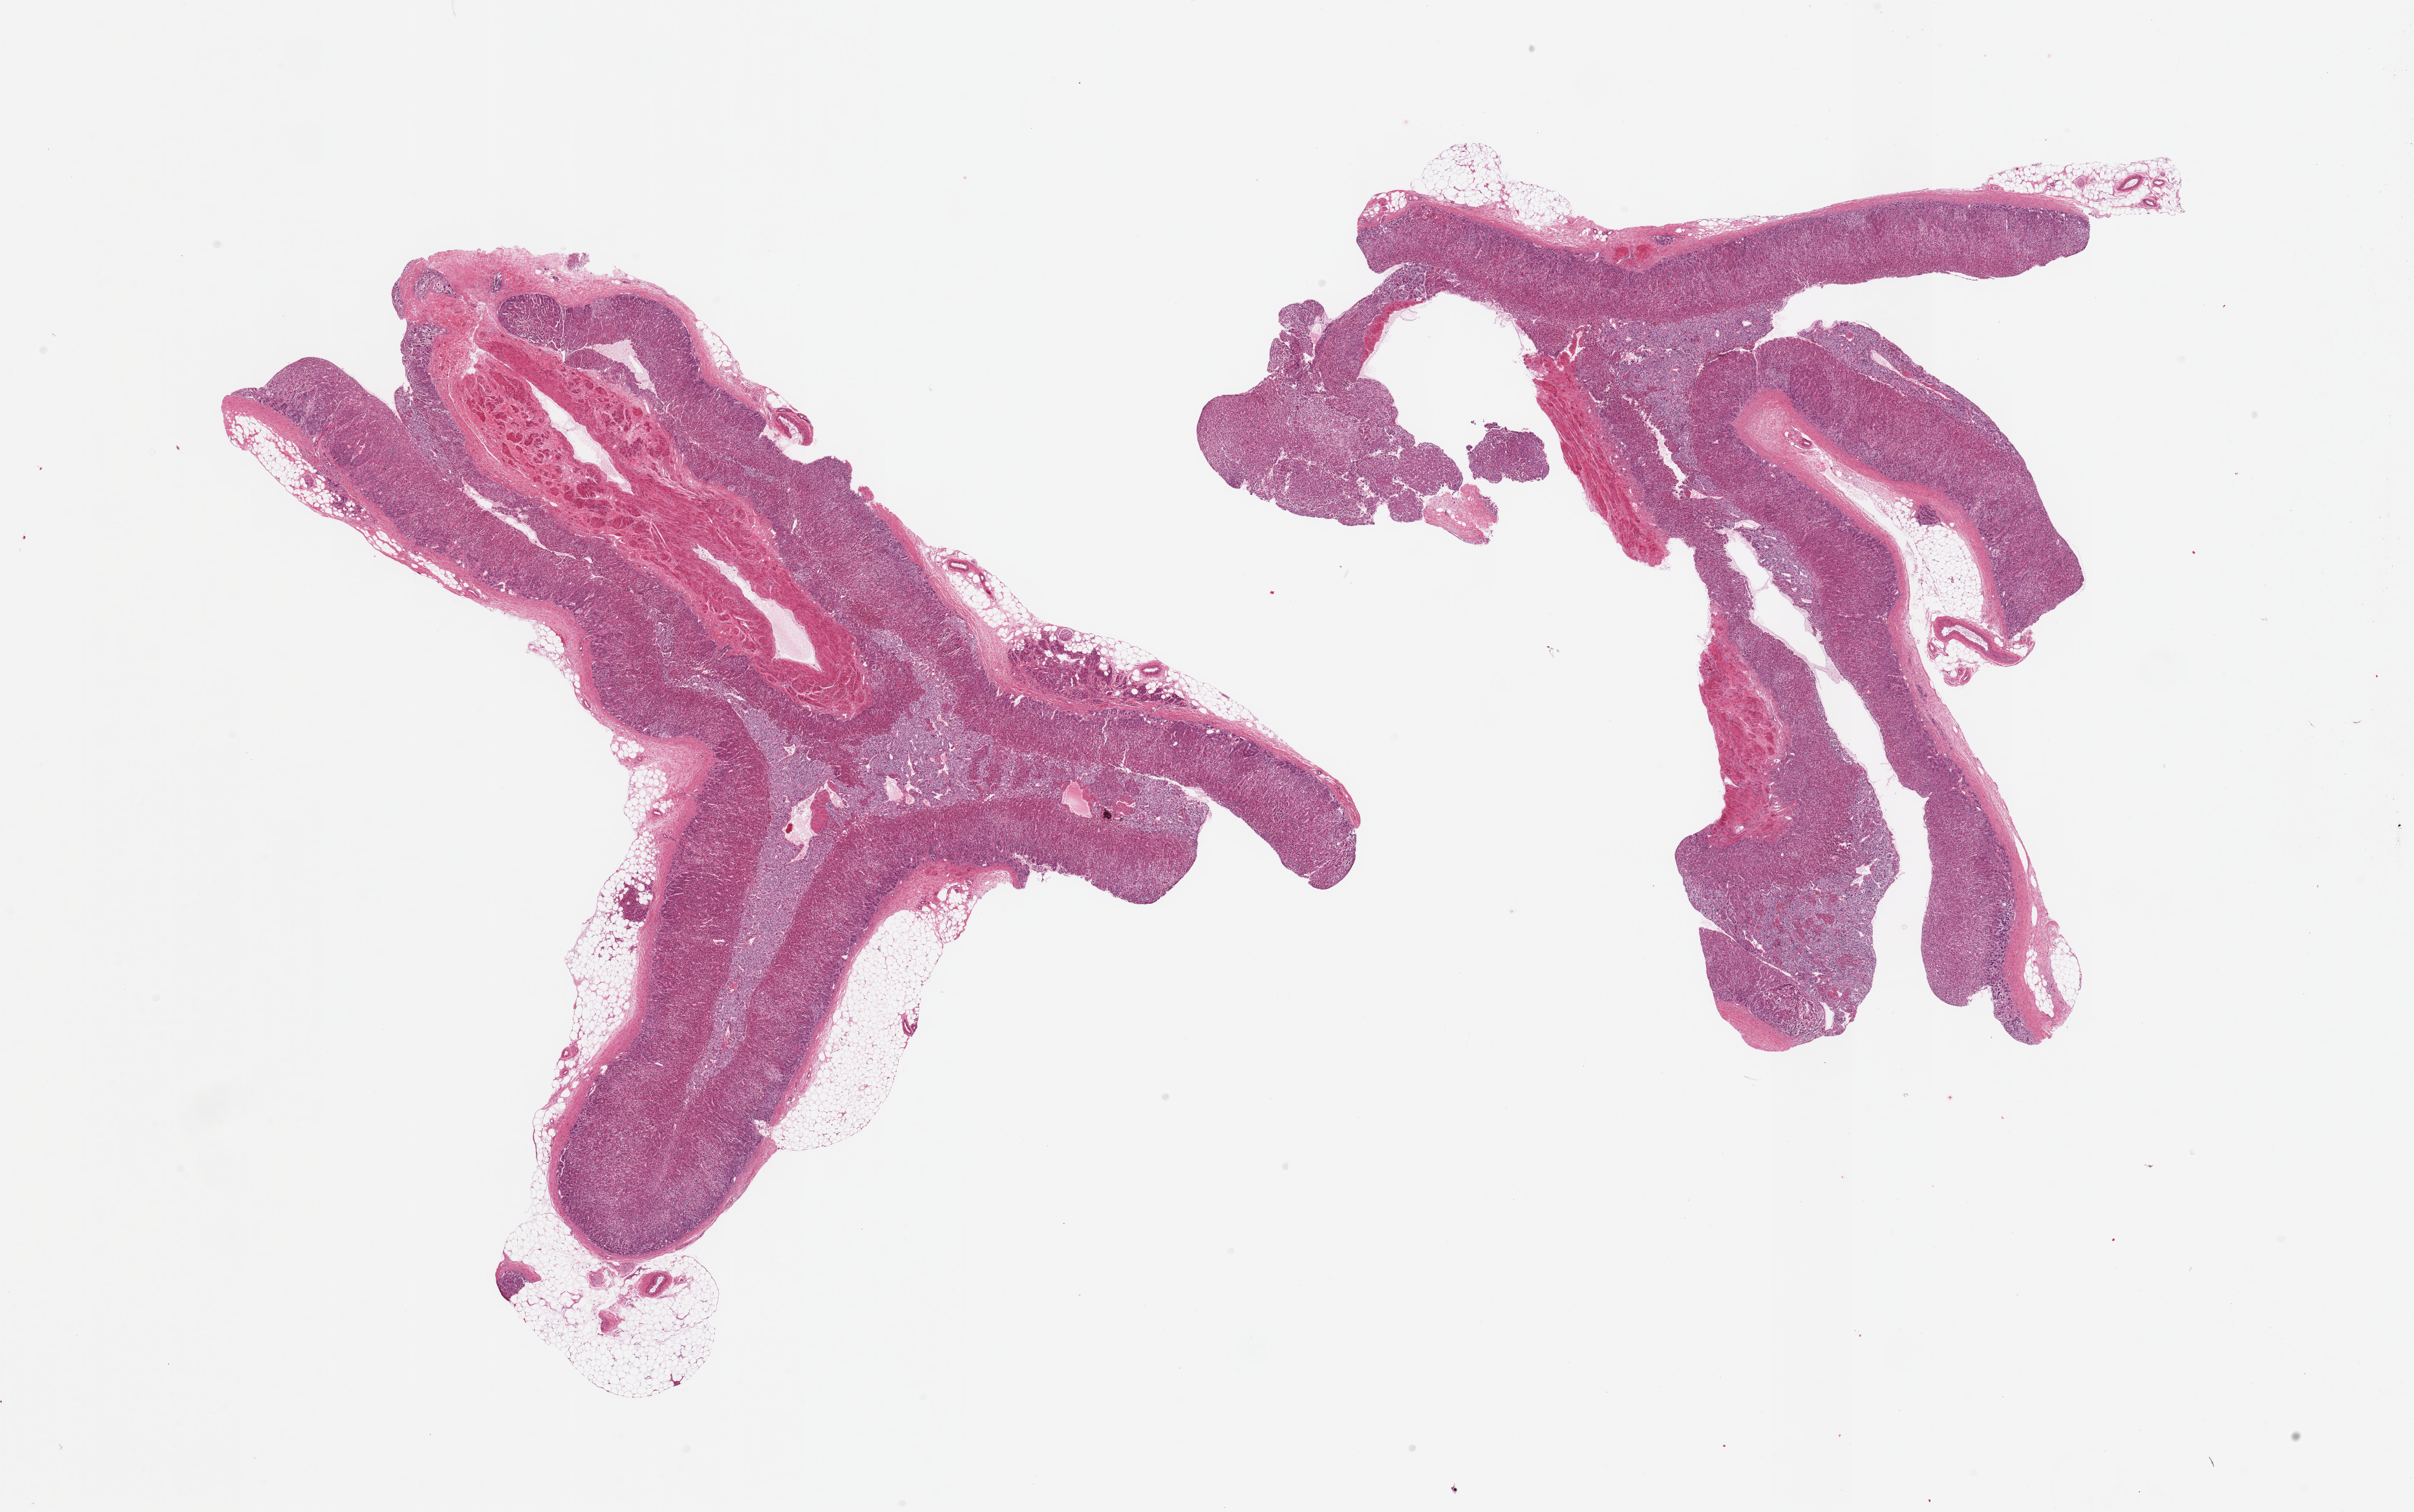
H&E whole-slide image, brightfield — a low-resolution overview of the entire scanned area, about 29.5 x 18.5 mm (from a 20x scan); PAXgene-fixed, paraffin-embedded tissue; section of adrenal gland (target tissue); tissue donor sample. Donor sex: male.
Pathologist's review note for this sample: 2 pieces; cortex and medulla and prominent vein; ~1mm rim of fat.